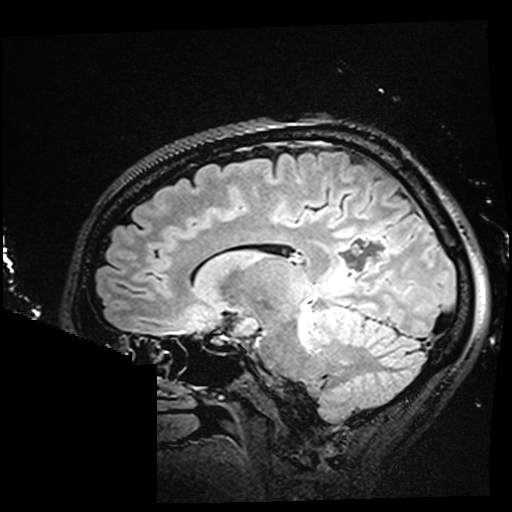
Brain MRI from a brain-tumour surgery series, one sagittal slice; slice 103 of 176 in the series (ordered by position); T2 FLAIR; 1 mm slice thickness; 512 × 512 image matrix, field of view 250 × 250 mm. From the clinical record (not read from this slice): histopathology: Oligodendroglioma; WHO grade: 2; IDH mutation: yes; tumour location: Right Parietal.
Annotated regions visible in this slice (manually delineated by an expert):
- residual tumour: bounding box (x1, y1, x2, y2) in pixels: (323, 267, 357, 296)